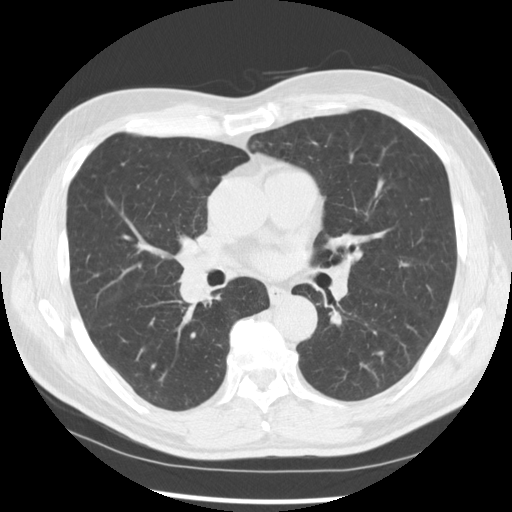
Chest CT (low-dose screening protocol), one axial image, baseline screening round, lung window (W 1500 / L -600 HU), standard (soft-tissue) reconstruction kernel (STANDARD). Male, age 67 years at enrolment. Current smoker at enrolment.
Lesion marked by an expert reader, bounding box [x1, y1, x2, y2] px = [160, 248, 229, 312]. Screening reader's record for this exam (one nodule recorded; not confirmed to be the boxed lesion): non-calcified nodule or mass ≥4 mm, left lower lobe, 15 × 15 mm, spiculated (stellate) margins, soft tissue attenuation. Note: the box lies in the patient's right hemithorax on this image, whereas the reader's record names the left lung; they may be different findings. Official screen result: positive, change unspecified: nodule(s) >= 4 mm or enlarging nodule(s), mass(es), or other non-specific abnormalities suspicious for lung cancer.